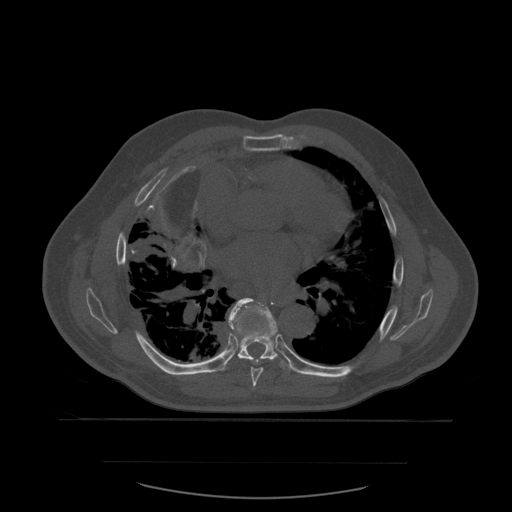
CT including the spine, one axial slice. Slice 372 of 590 in the series (ordered by position). Bone window (W 1800 / L 400 HU). 1.25 mm slice thickness. 512 × 512 image matrix. Patient age 71 years. From the clinical record (not read from this slice): primary cancer: lung; vertebrae with lytic lesions (as recorded): T1, T2, L5, S1.
Annotated regions visible in this slice (semi-automatic segmentation, software-assisted and operator-edited):
- T7 vertebra: bounding box [x1, y1, x2, y2] px = [231, 298, 264, 390]
- T8 vertebra: [228, 299, 293, 371]